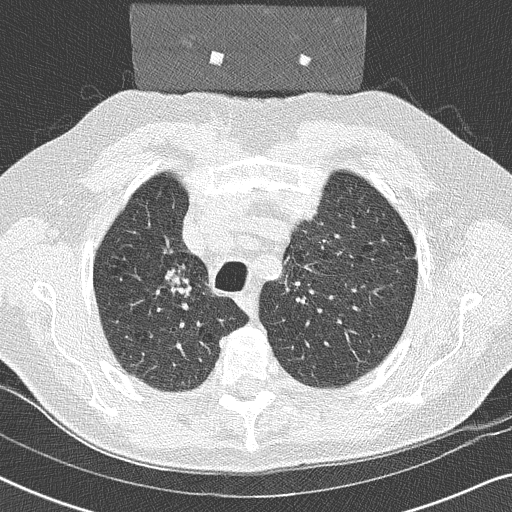
Low-dose screening chest CT, one axial slice; position 186 of 252 along the scan axis; lung window (W 1500 / L -600 HU); 2 mm slice thickness; 512 × 512 image matrix, field of view 330 × 330 mm.
Structures marked on this image (manually delineated by an expert):
- lesion 1 (tumor, upper lobe of right lung): bounding box <170,275,181,288> (left, top, right, bottom; pixels)